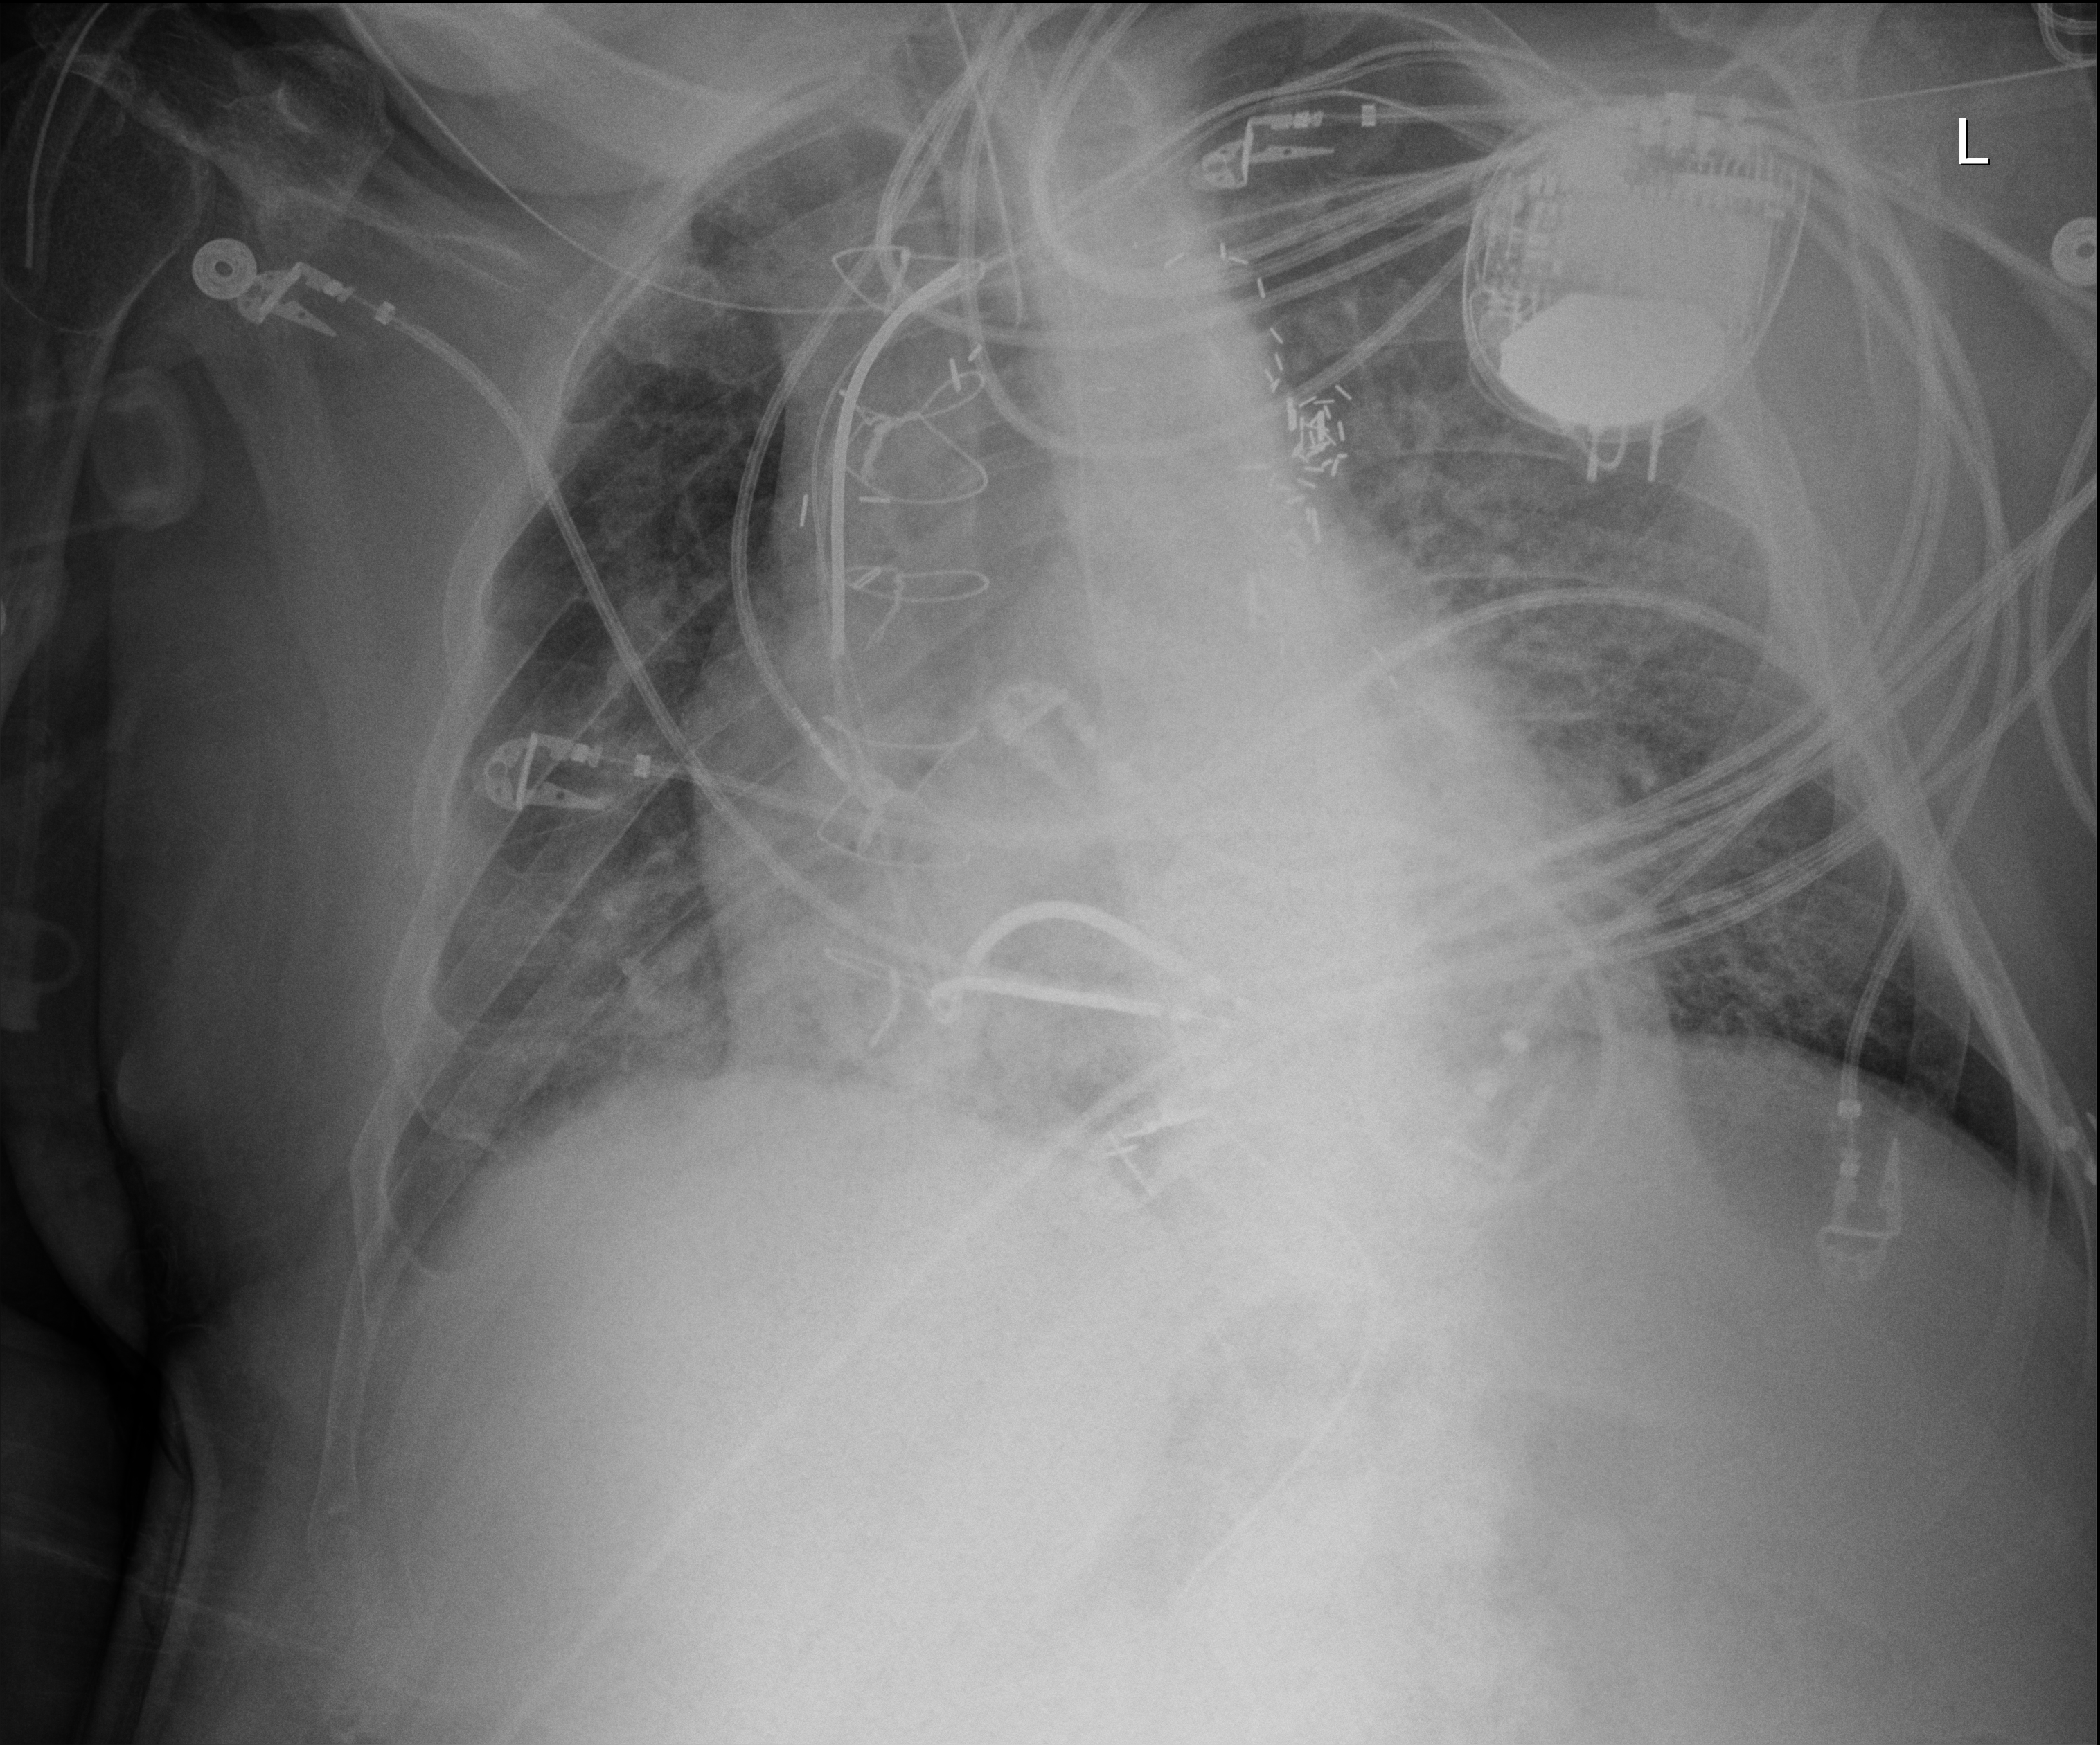
Bedside chest radiograph (digital radiography). Patient hospitalised with COVID-19; male, aged 60–74 years.
Hospital-stay facts (about this admission, not read from this image; timing relative to this image not recorded): smoking status (admission record): never.